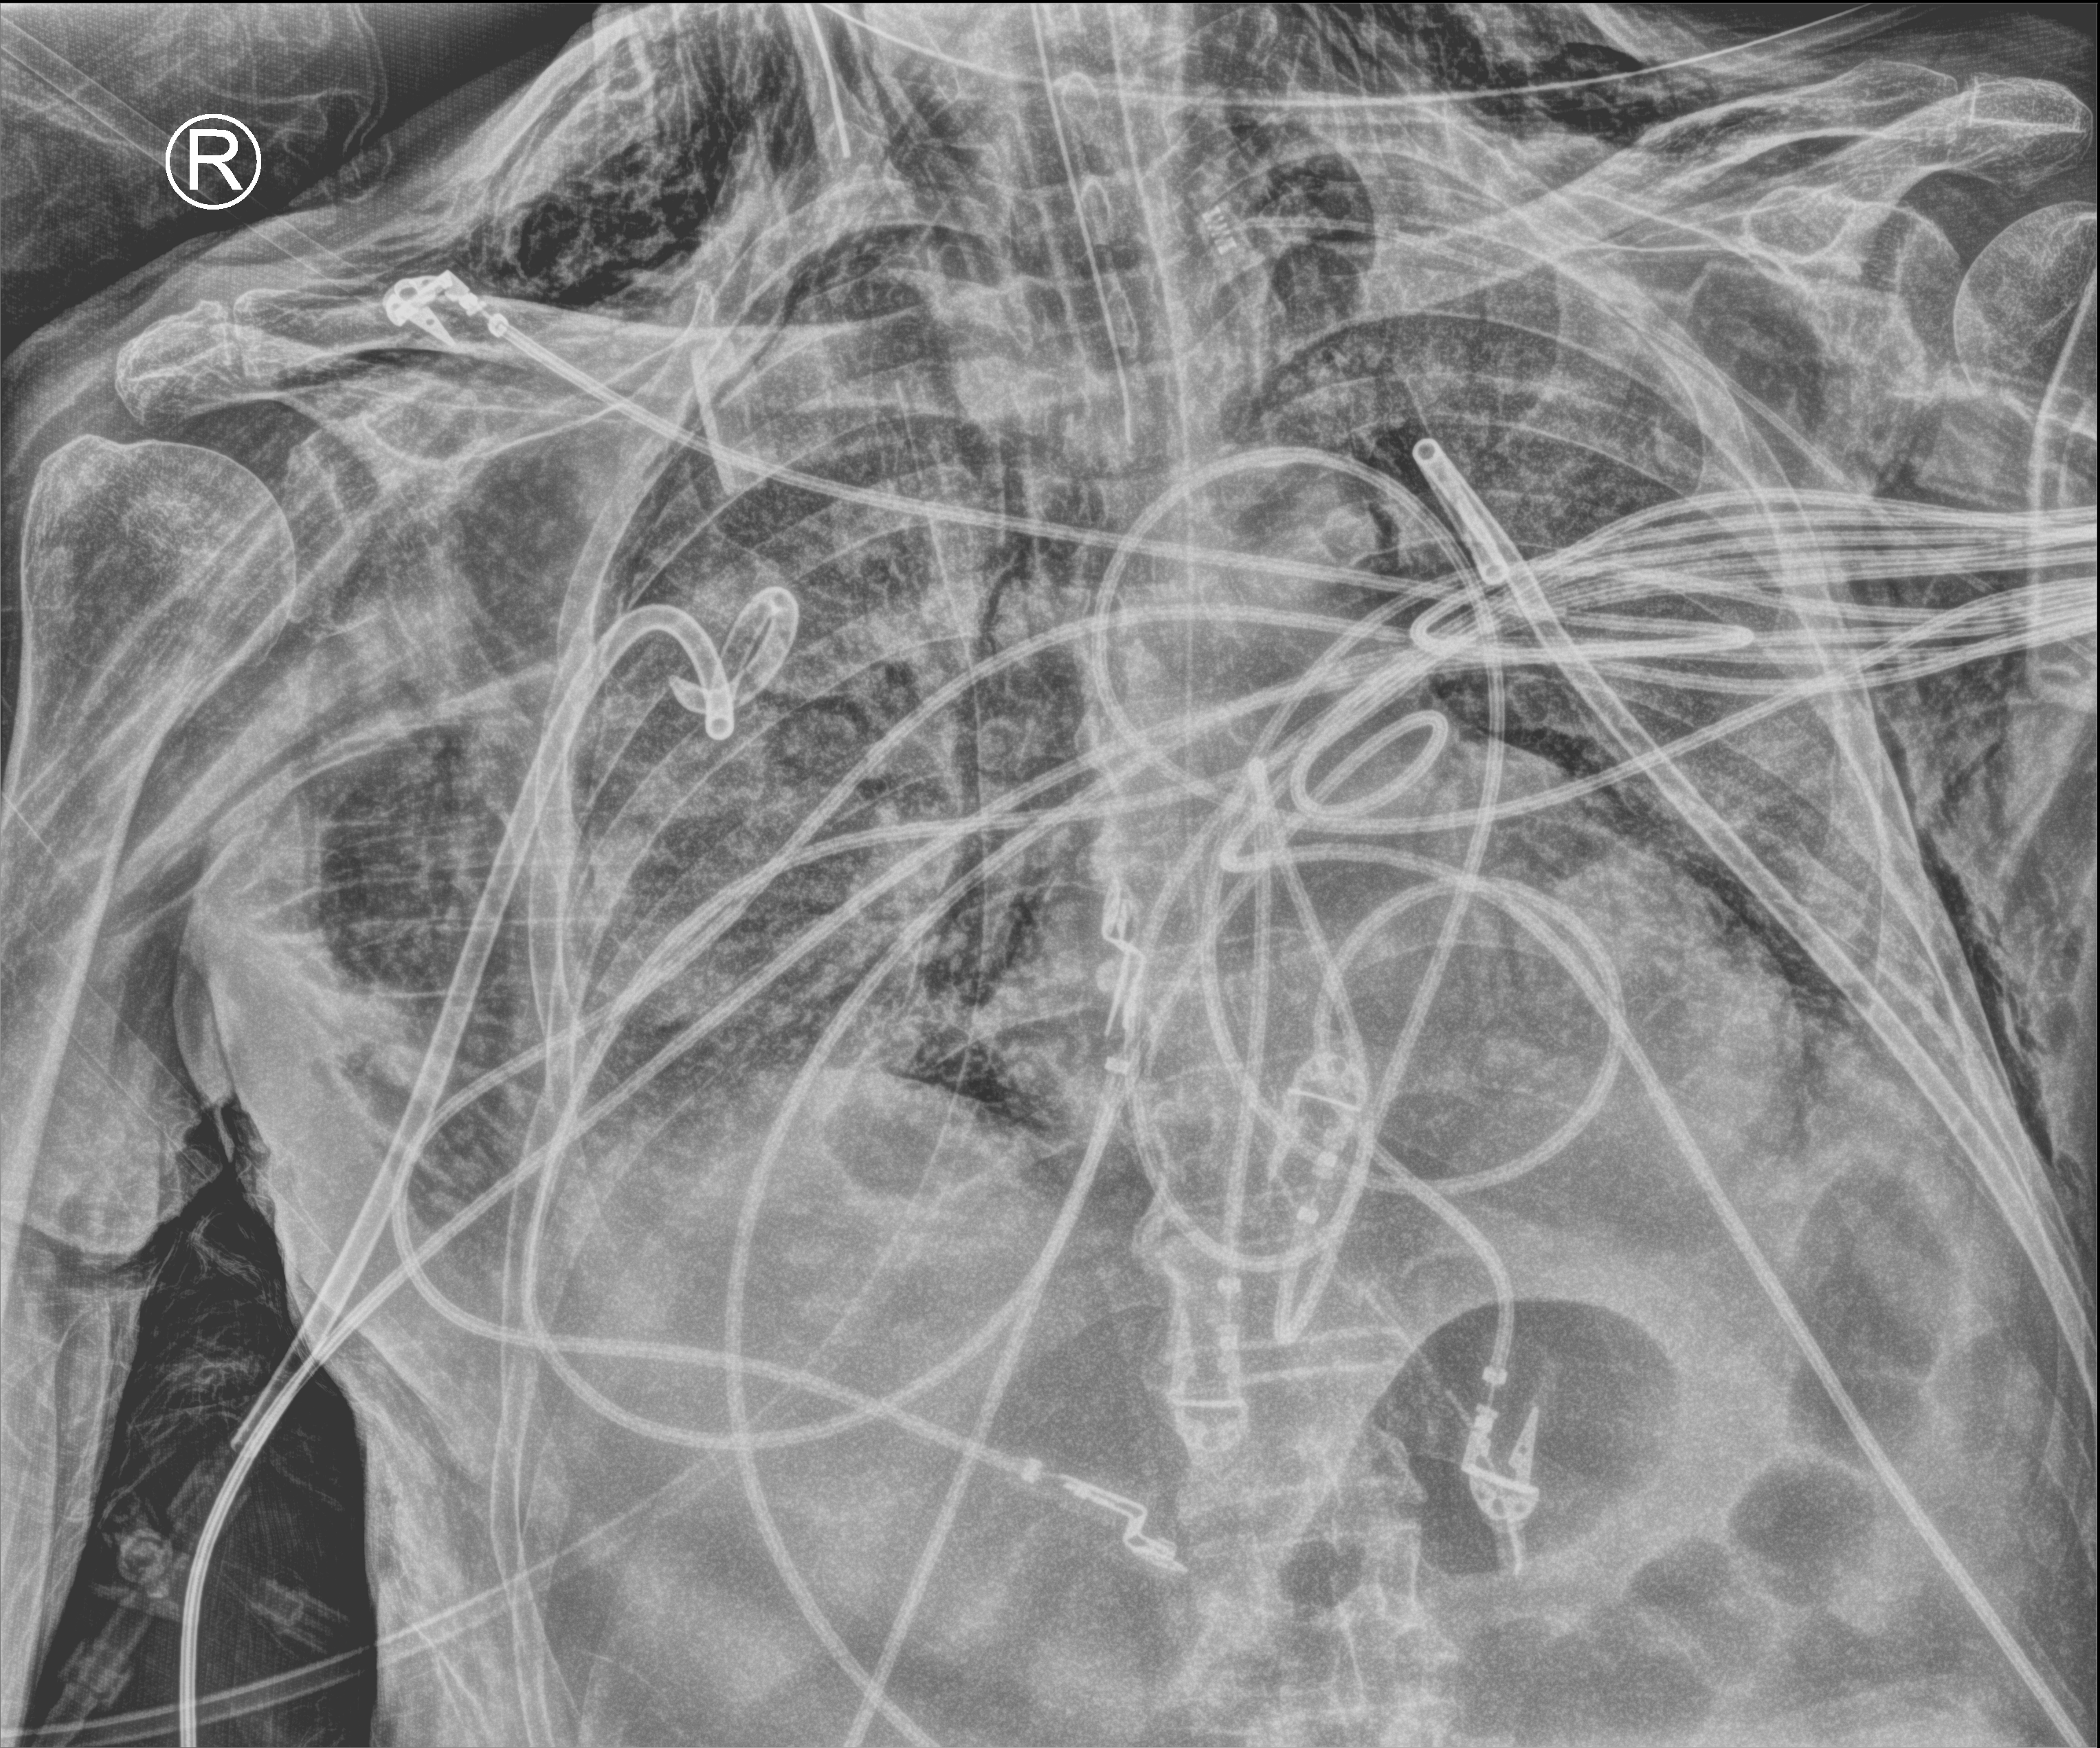
Bedside chest radiograph (computed radiography). Patient hospitalised with COVID-19; male, aged 75–90 years.
Hospital-stay facts (about this admission, not read from this image; timing relative to this image not recorded):
- mechanically ventilated during this hospital stay: yes